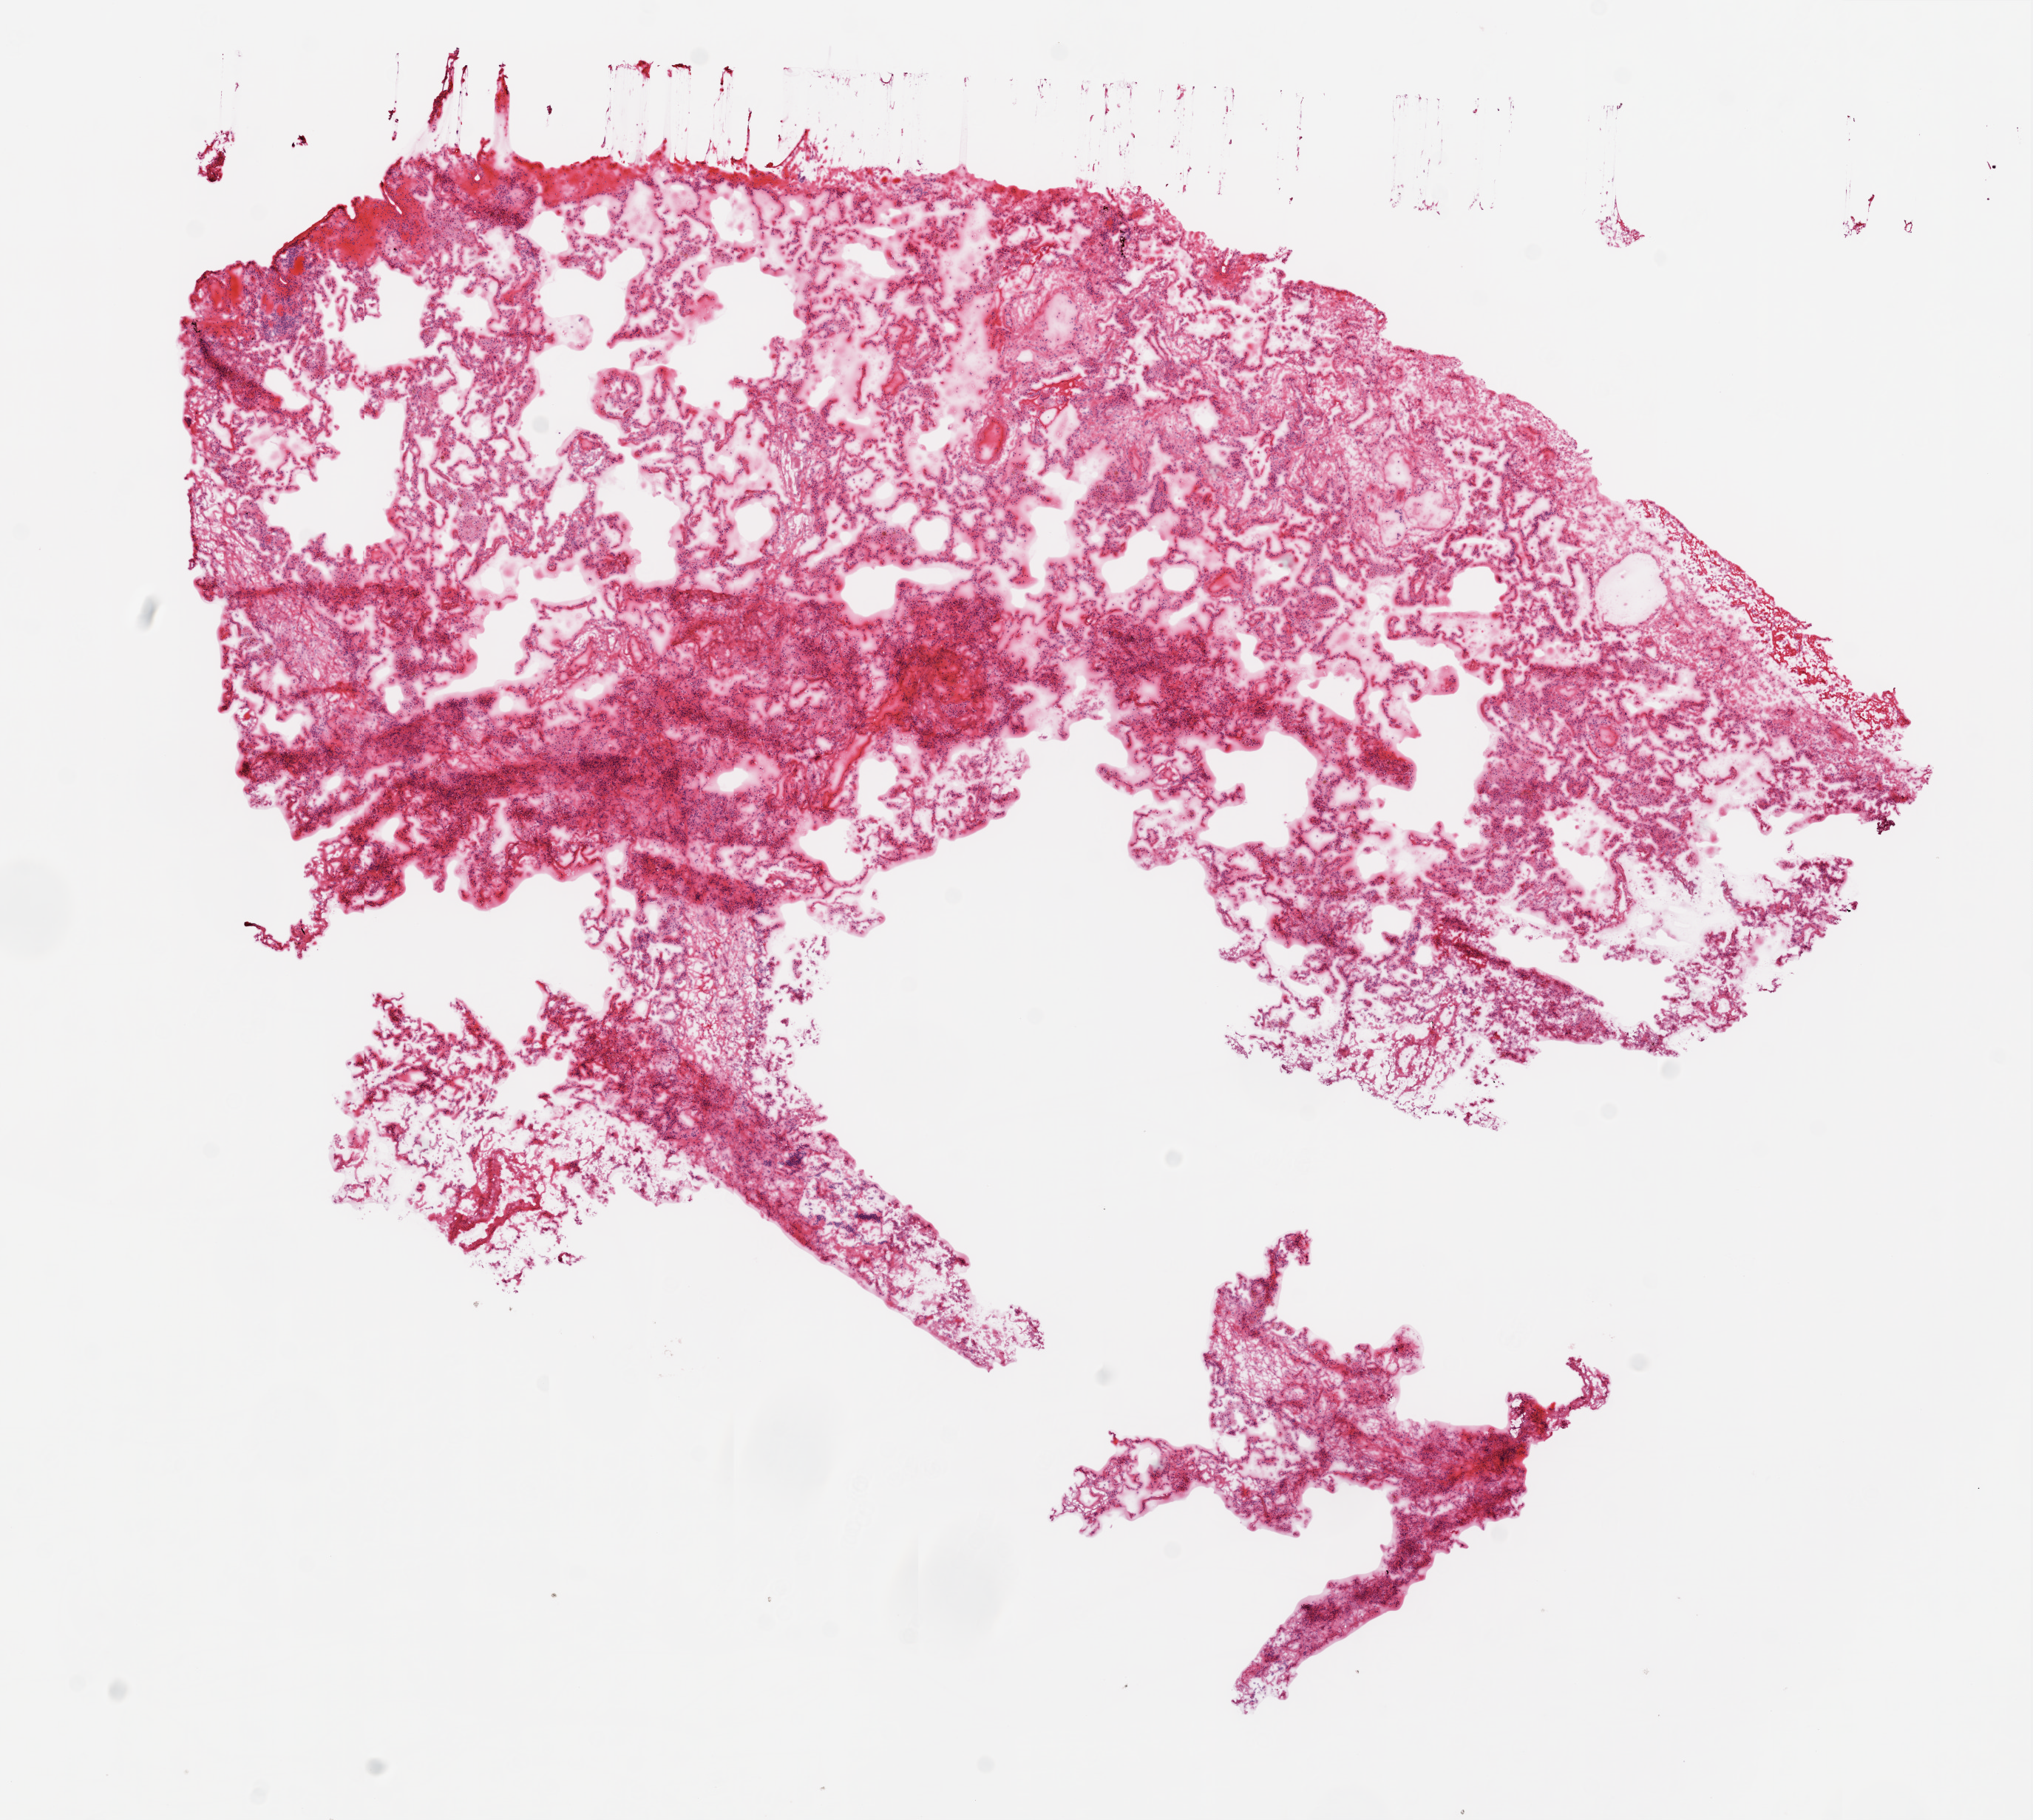
Digitized H&E tissue section (whole slide), low-resolution overview of the scanned area, about 11.0 x 9.9 mm. Frozen section from the top of the tissue portion. Solid tissue normal (non-tumour tissue) sample from the lung. Patient: male, age at initial diagnosis 74 years.
This section: solid tissue normal sample (biorepository sample class). Patient diagnosis: Squamous cell carcinoma, NOS (upper lobe, lung).